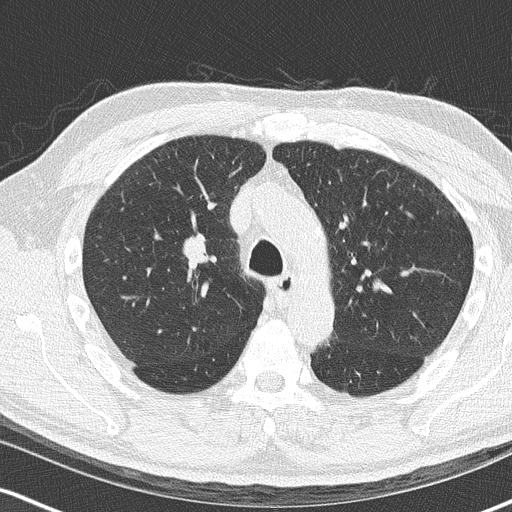
Low-dose screening chest CT, axial slice. Second screening round (one year after baseline). Lung window (W 1500 / L -600 HU). 2 mm slice thickness. Slice 62 of 170 in the series. Male participant, aged 68 years at enrolment. Current smoker at enrolment.
Expert-annotated lung lesion, box from (x=152, y=222) to (x=217, y=286) px. The exam's reader record, not a measurement of the box and not confirmed to be the same lesion: non-calcified nodule or mass ≥4 mm, right upper lobe, 18 × 15 mm, smooth margins, soft tissue attenuation, pre-existing on the prior screen: no.